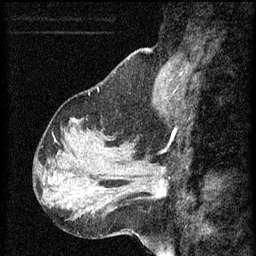
Breast MRI (dynamic contrast-enhanced), one sagittal slice; position 20 of 60 along the scan axis; 3 images stored at this slice position (order not interpretable as contrast timing); 1.5 T; TE 4.2 ms, TR 8.2 ms; 256 × 256 image matrix, field of view 180 × 180 mm. Patient: female, 37 years.
Outlined on this slice (semi-automatically segmented with operator editing):
- analysis volume of interest (the breast-tissue region the enhancement analysis was run in; not a lesion): box from (x=126, y=156) to (x=180, y=205) px
- tumour enhancement mask (voxels above the 70 % enhancement threshold inside the analysis volume of interest): (x=154, y=168)–(x=166, y=197)